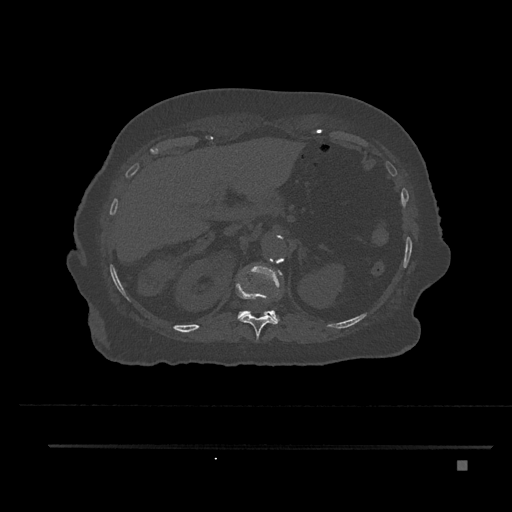
CT including the spine, one axial slice. Slice 295 of 797 in the series (ordered by position). Reconstruction kernel Br40s/3. Bone window (W 1800 / L 400 HU). 0.5 mm slice thickness. 512 × 512 image matrix. Female patient, age 76 years. From the clinical record (not read from this slice): primary cancer: lung.
Outlined on this slice (semi-automatic segmentation, software-assisted and operator-edited):
- T11 vertebra: box from (x=236, y=285) to (x=279, y=339) px
- T12 vertebra: (x=237, y=266)–(x=280, y=322)